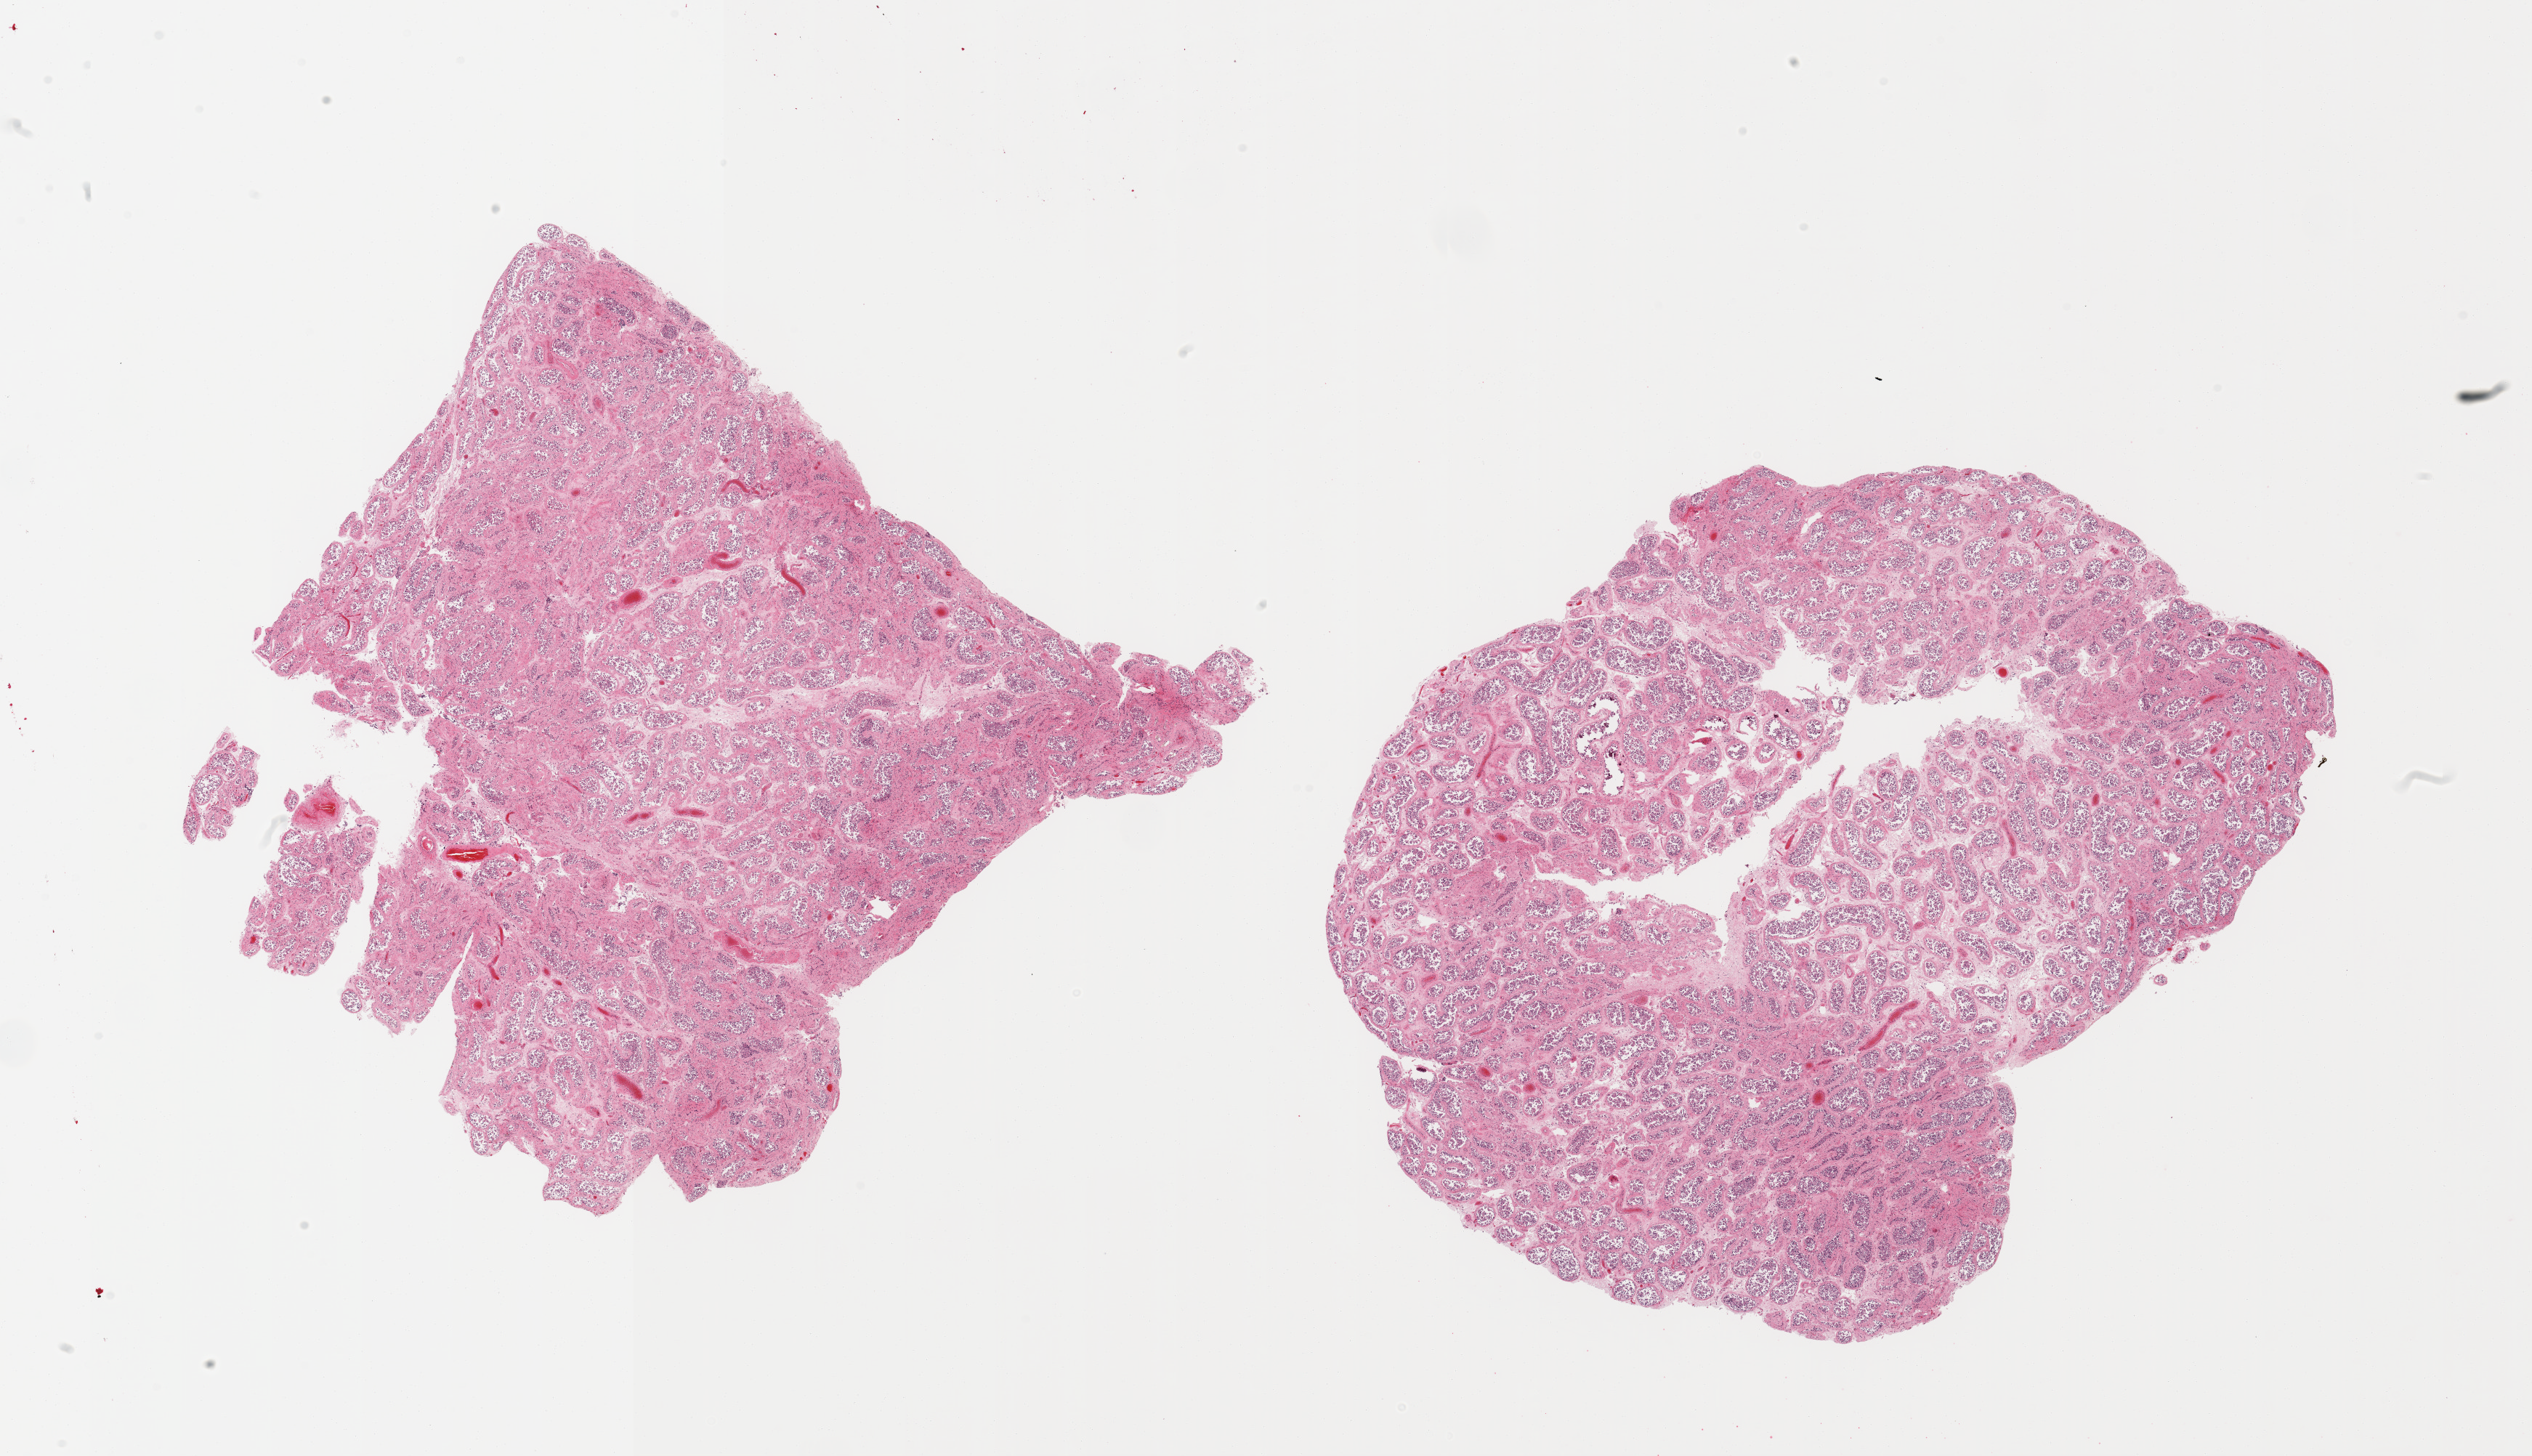
Whole-slide image, haematoxylin and eosin stain, brightfield, whole scanned area (about 27.6 x 15.9 mm) shown as a low-resolution overview; PAXgene-fixed paraffin-embedded (PFPE) section; sampled site (target tissue): testis; tissue donor sample.
Reviewer comment on this tissue sample: 2 pieces, advanced autolysis.